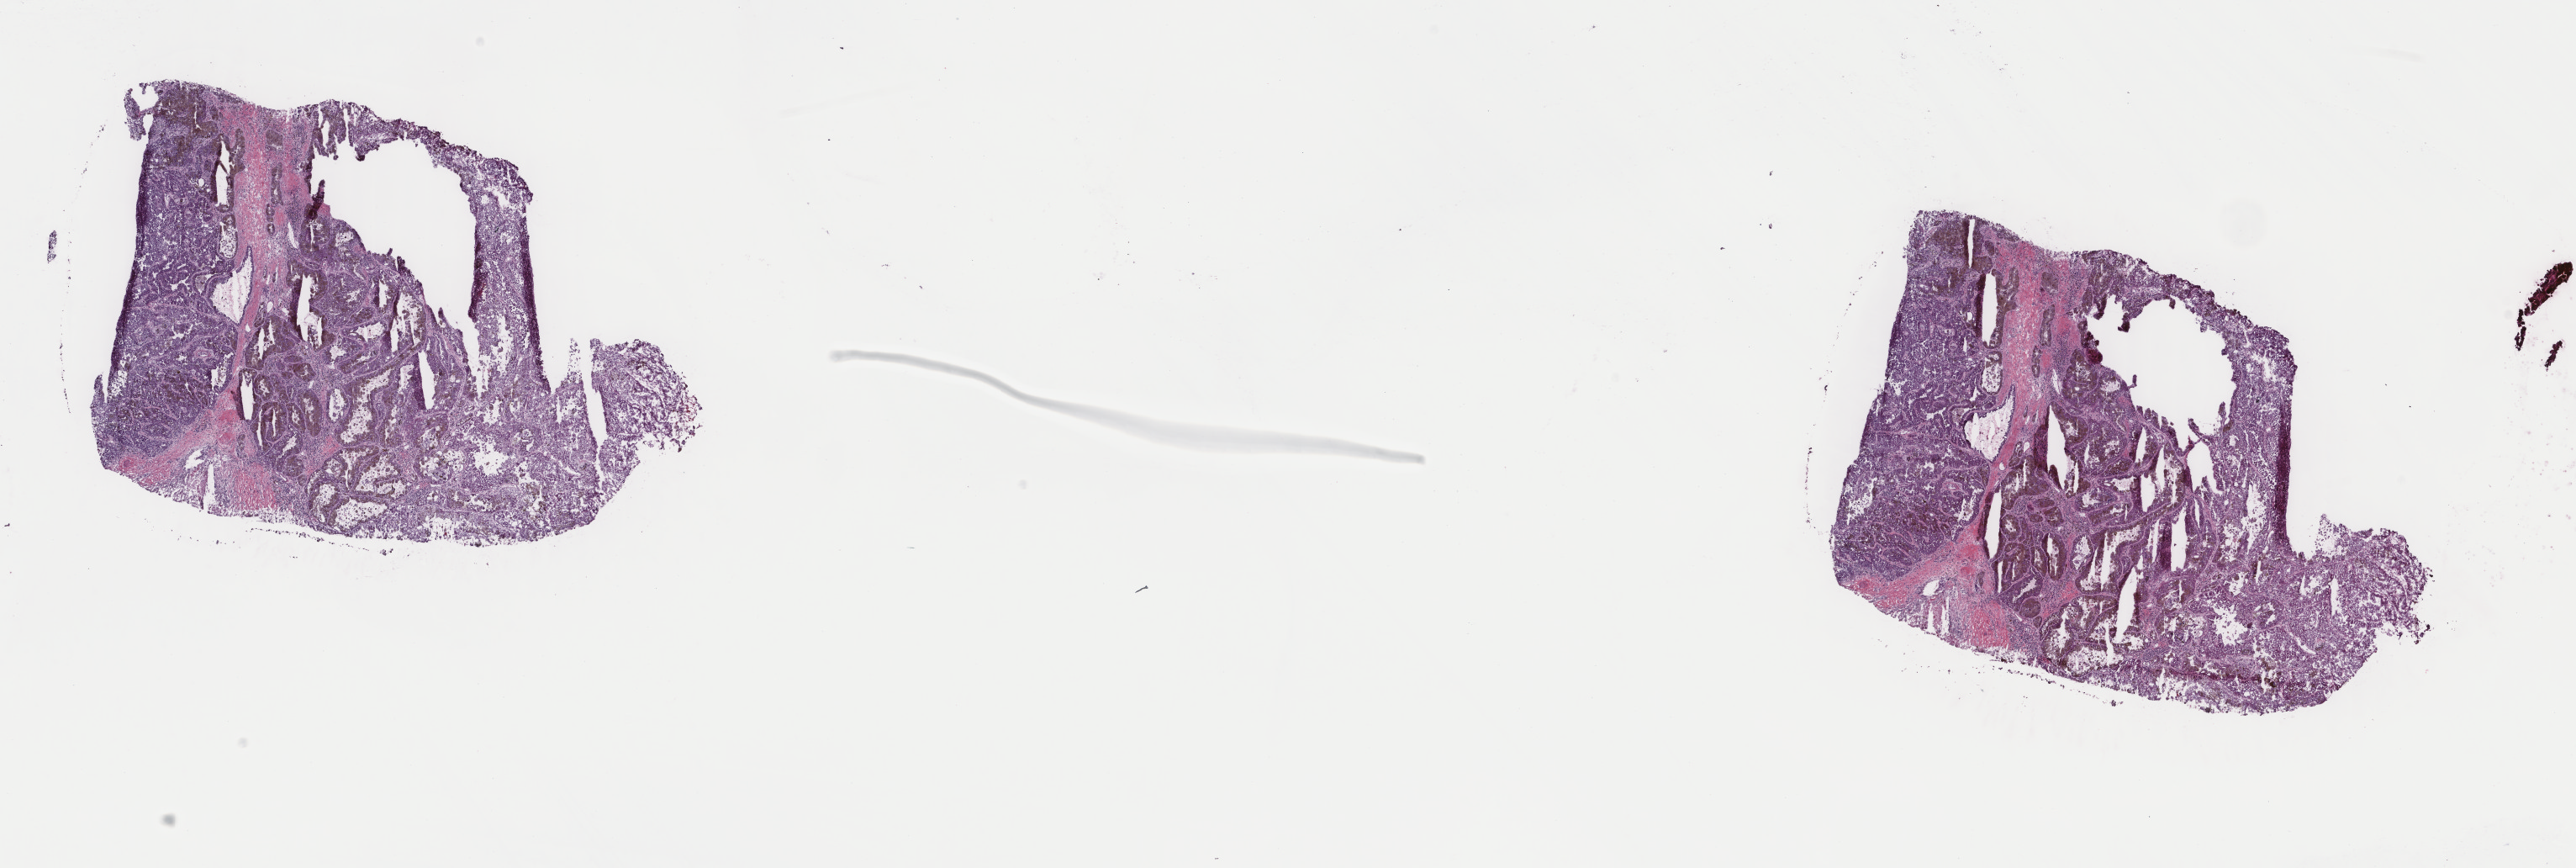
Digitized H&E-stained tissue section (whole slide), a low-resolution overview of the entire scanned area, about 24.3 x 8.2 mm; frozen section from the top of the tissue portion; sample: primary tumour, kidney. Male, age 61 years at initial diagnosis.
Histologic diagnosis: Papillary adenocarcinoma, NOS.